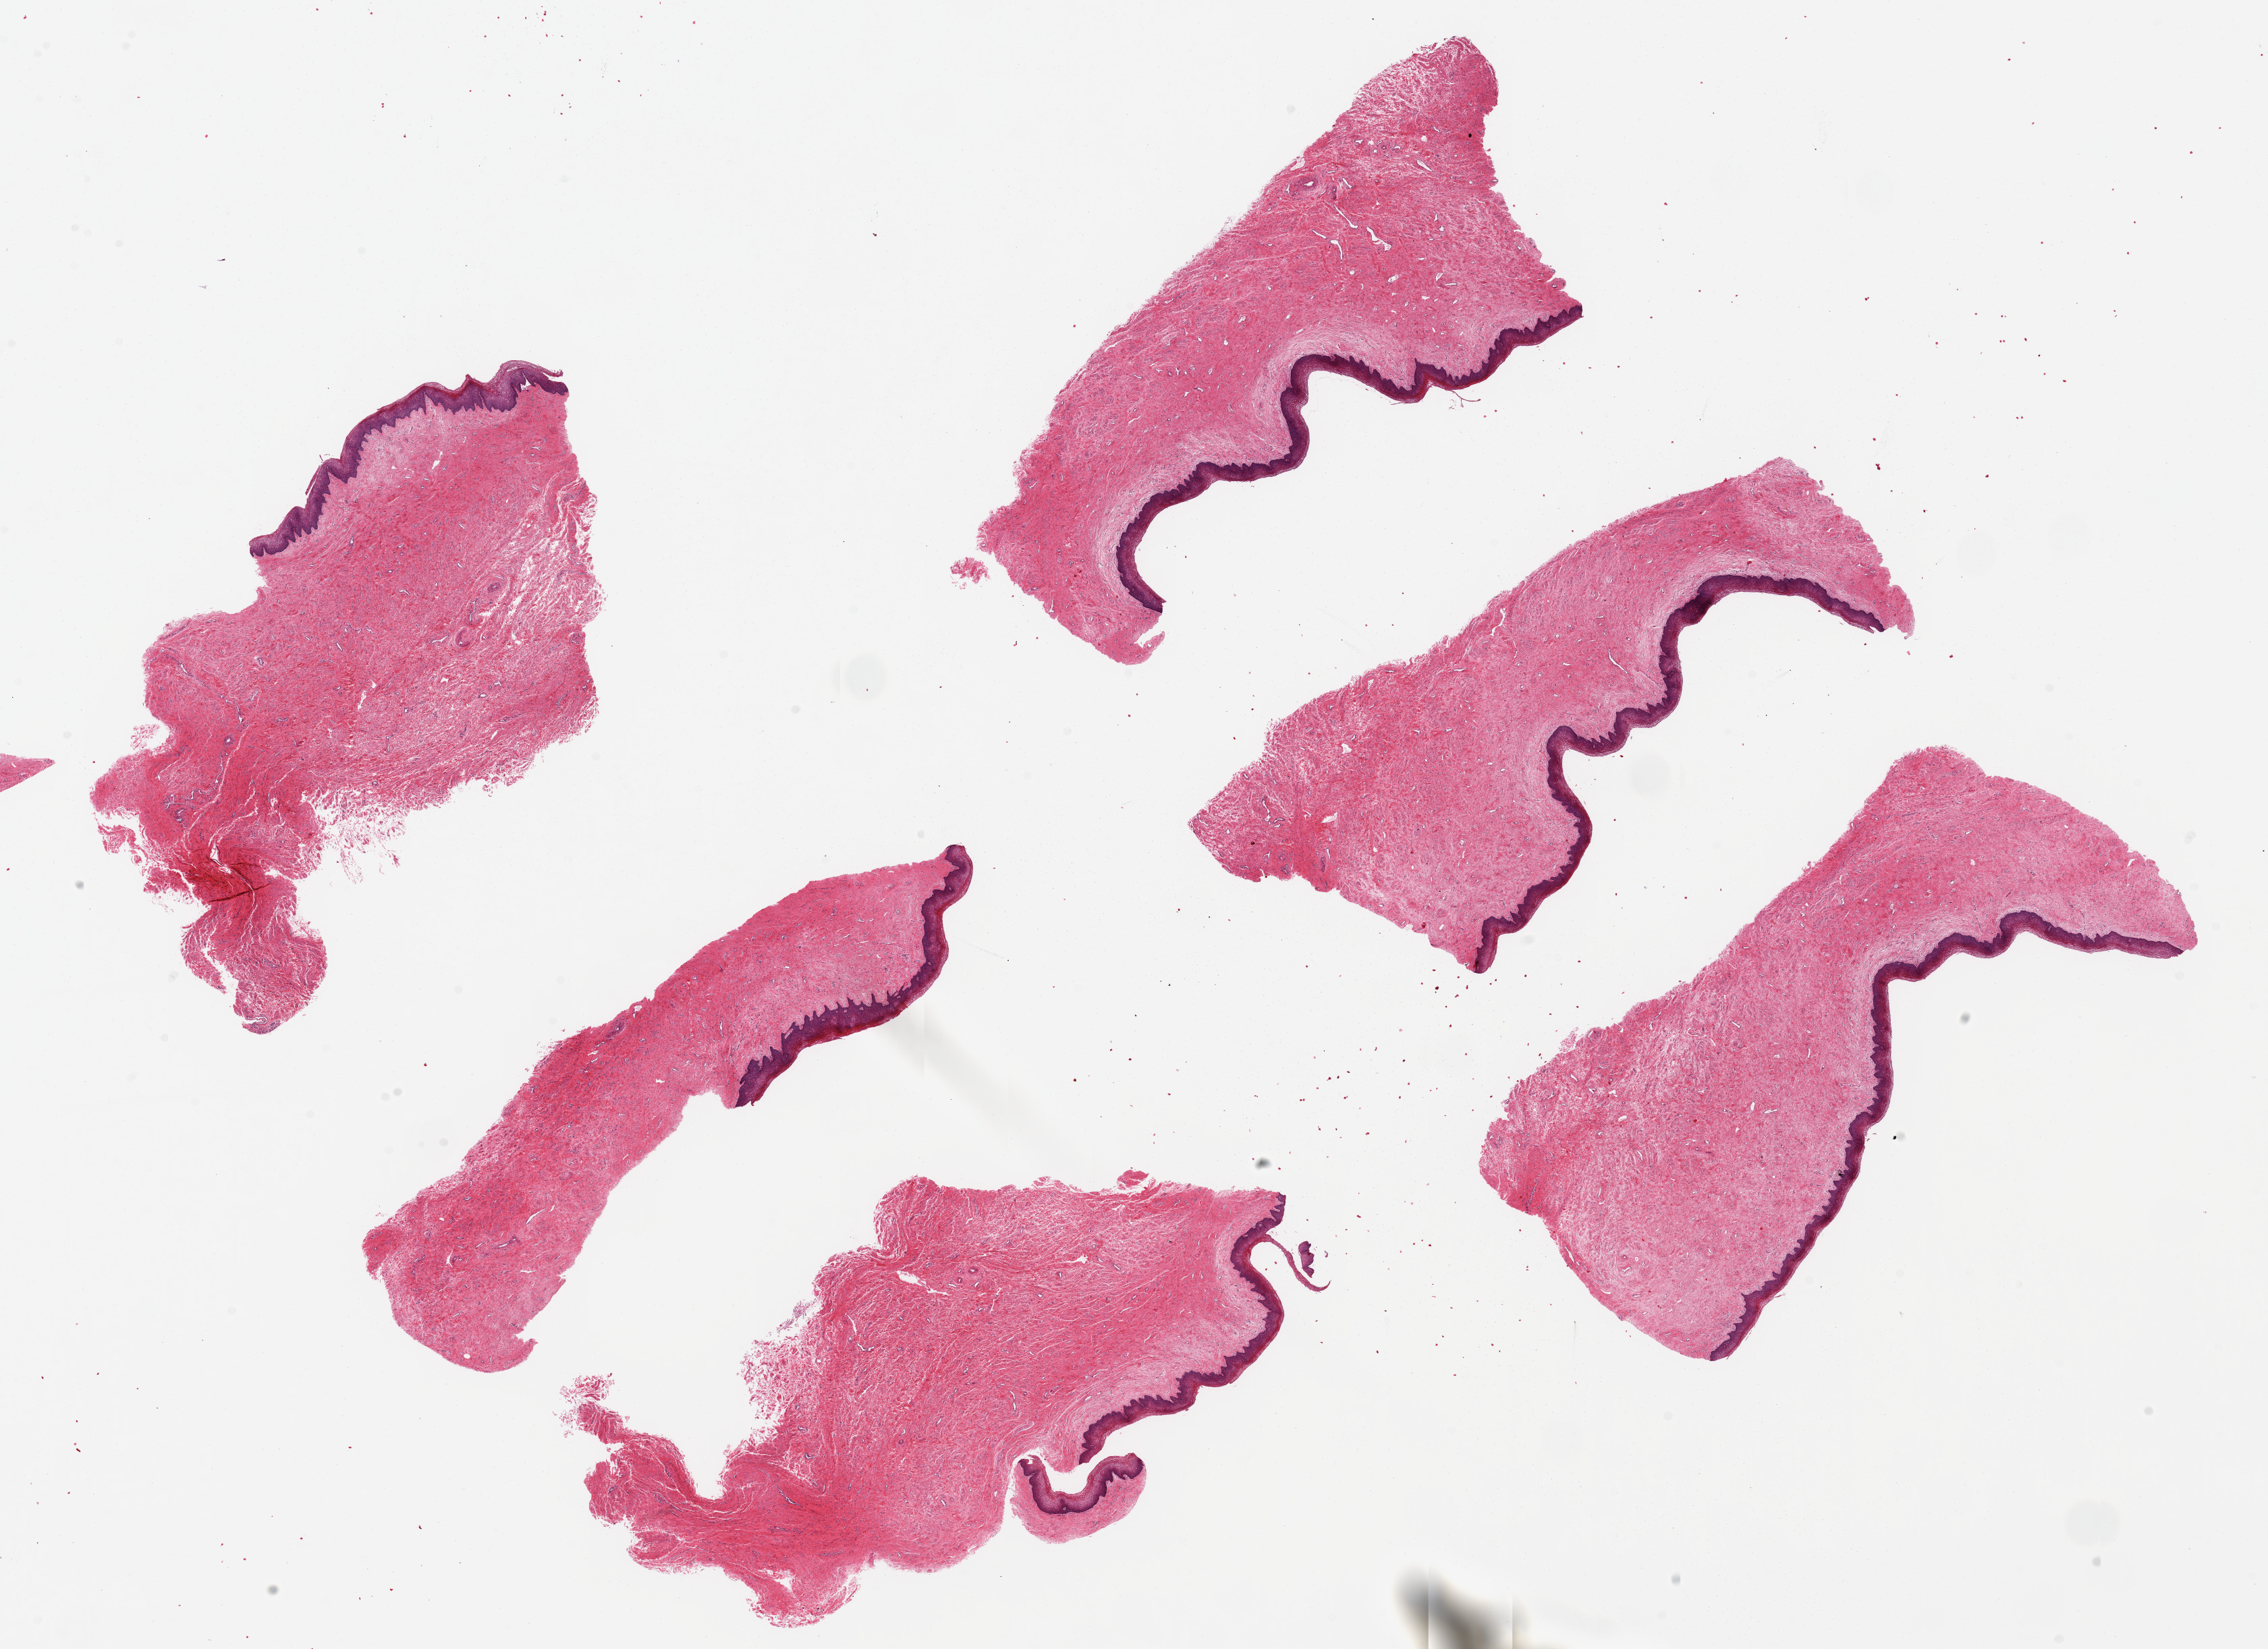
Digitized haematoxylin and eosin-stained section — shown as a low-resolution overview of the whole scanned area (about 26.6 x 19.3 mm). PAXgene-fixed paraffin-embedded (PFPE) section. Sampled site (target tissue): vagina. Tissue donor sample. Female donor.
* review note (as recorded): 6 pieces up to 7x3.5 mm; good epithelial preservation ~0.3 mm thick